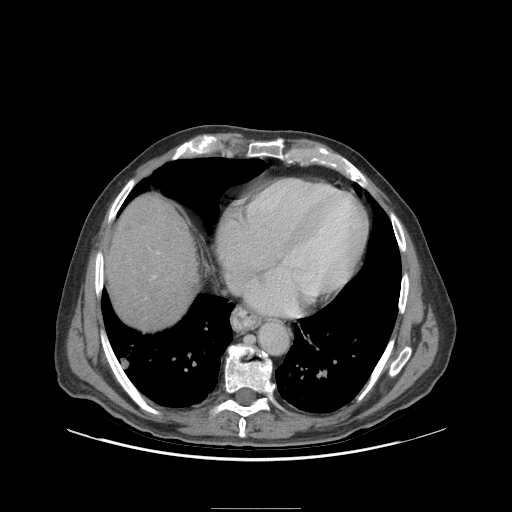
Contrast-enhanced abdominal CT (liver protocol), one axial slice. Position 91 of 105 along the scan axis. Reconstruction kernel STANDARD. Soft-tissue window (W 400 / L 40 HU). 2.5 mm slice thickness. 512 × 512 image matrix, field of view 440 × 440 mm. From the clinical record (not read from this slice): diagnosis: hepatocellular carcinoma (patient treated with transarterial chemoembolisation; whether this scan precedes or follows treatment is not stated here); TNM stage (as recorded): Stage-I; Child-Pugh class: A; tumour size: 5.1 cm.
Outlined on this slice (semi-automatic segmentation, software-assisted and operator-edited):
- liver parenchyma outside the tumour (the mass and vessels are separate outlines, so this box may not span the whole liver): bounding box (x1, y1, x2, y2) in pixels: (104, 194, 198, 328)